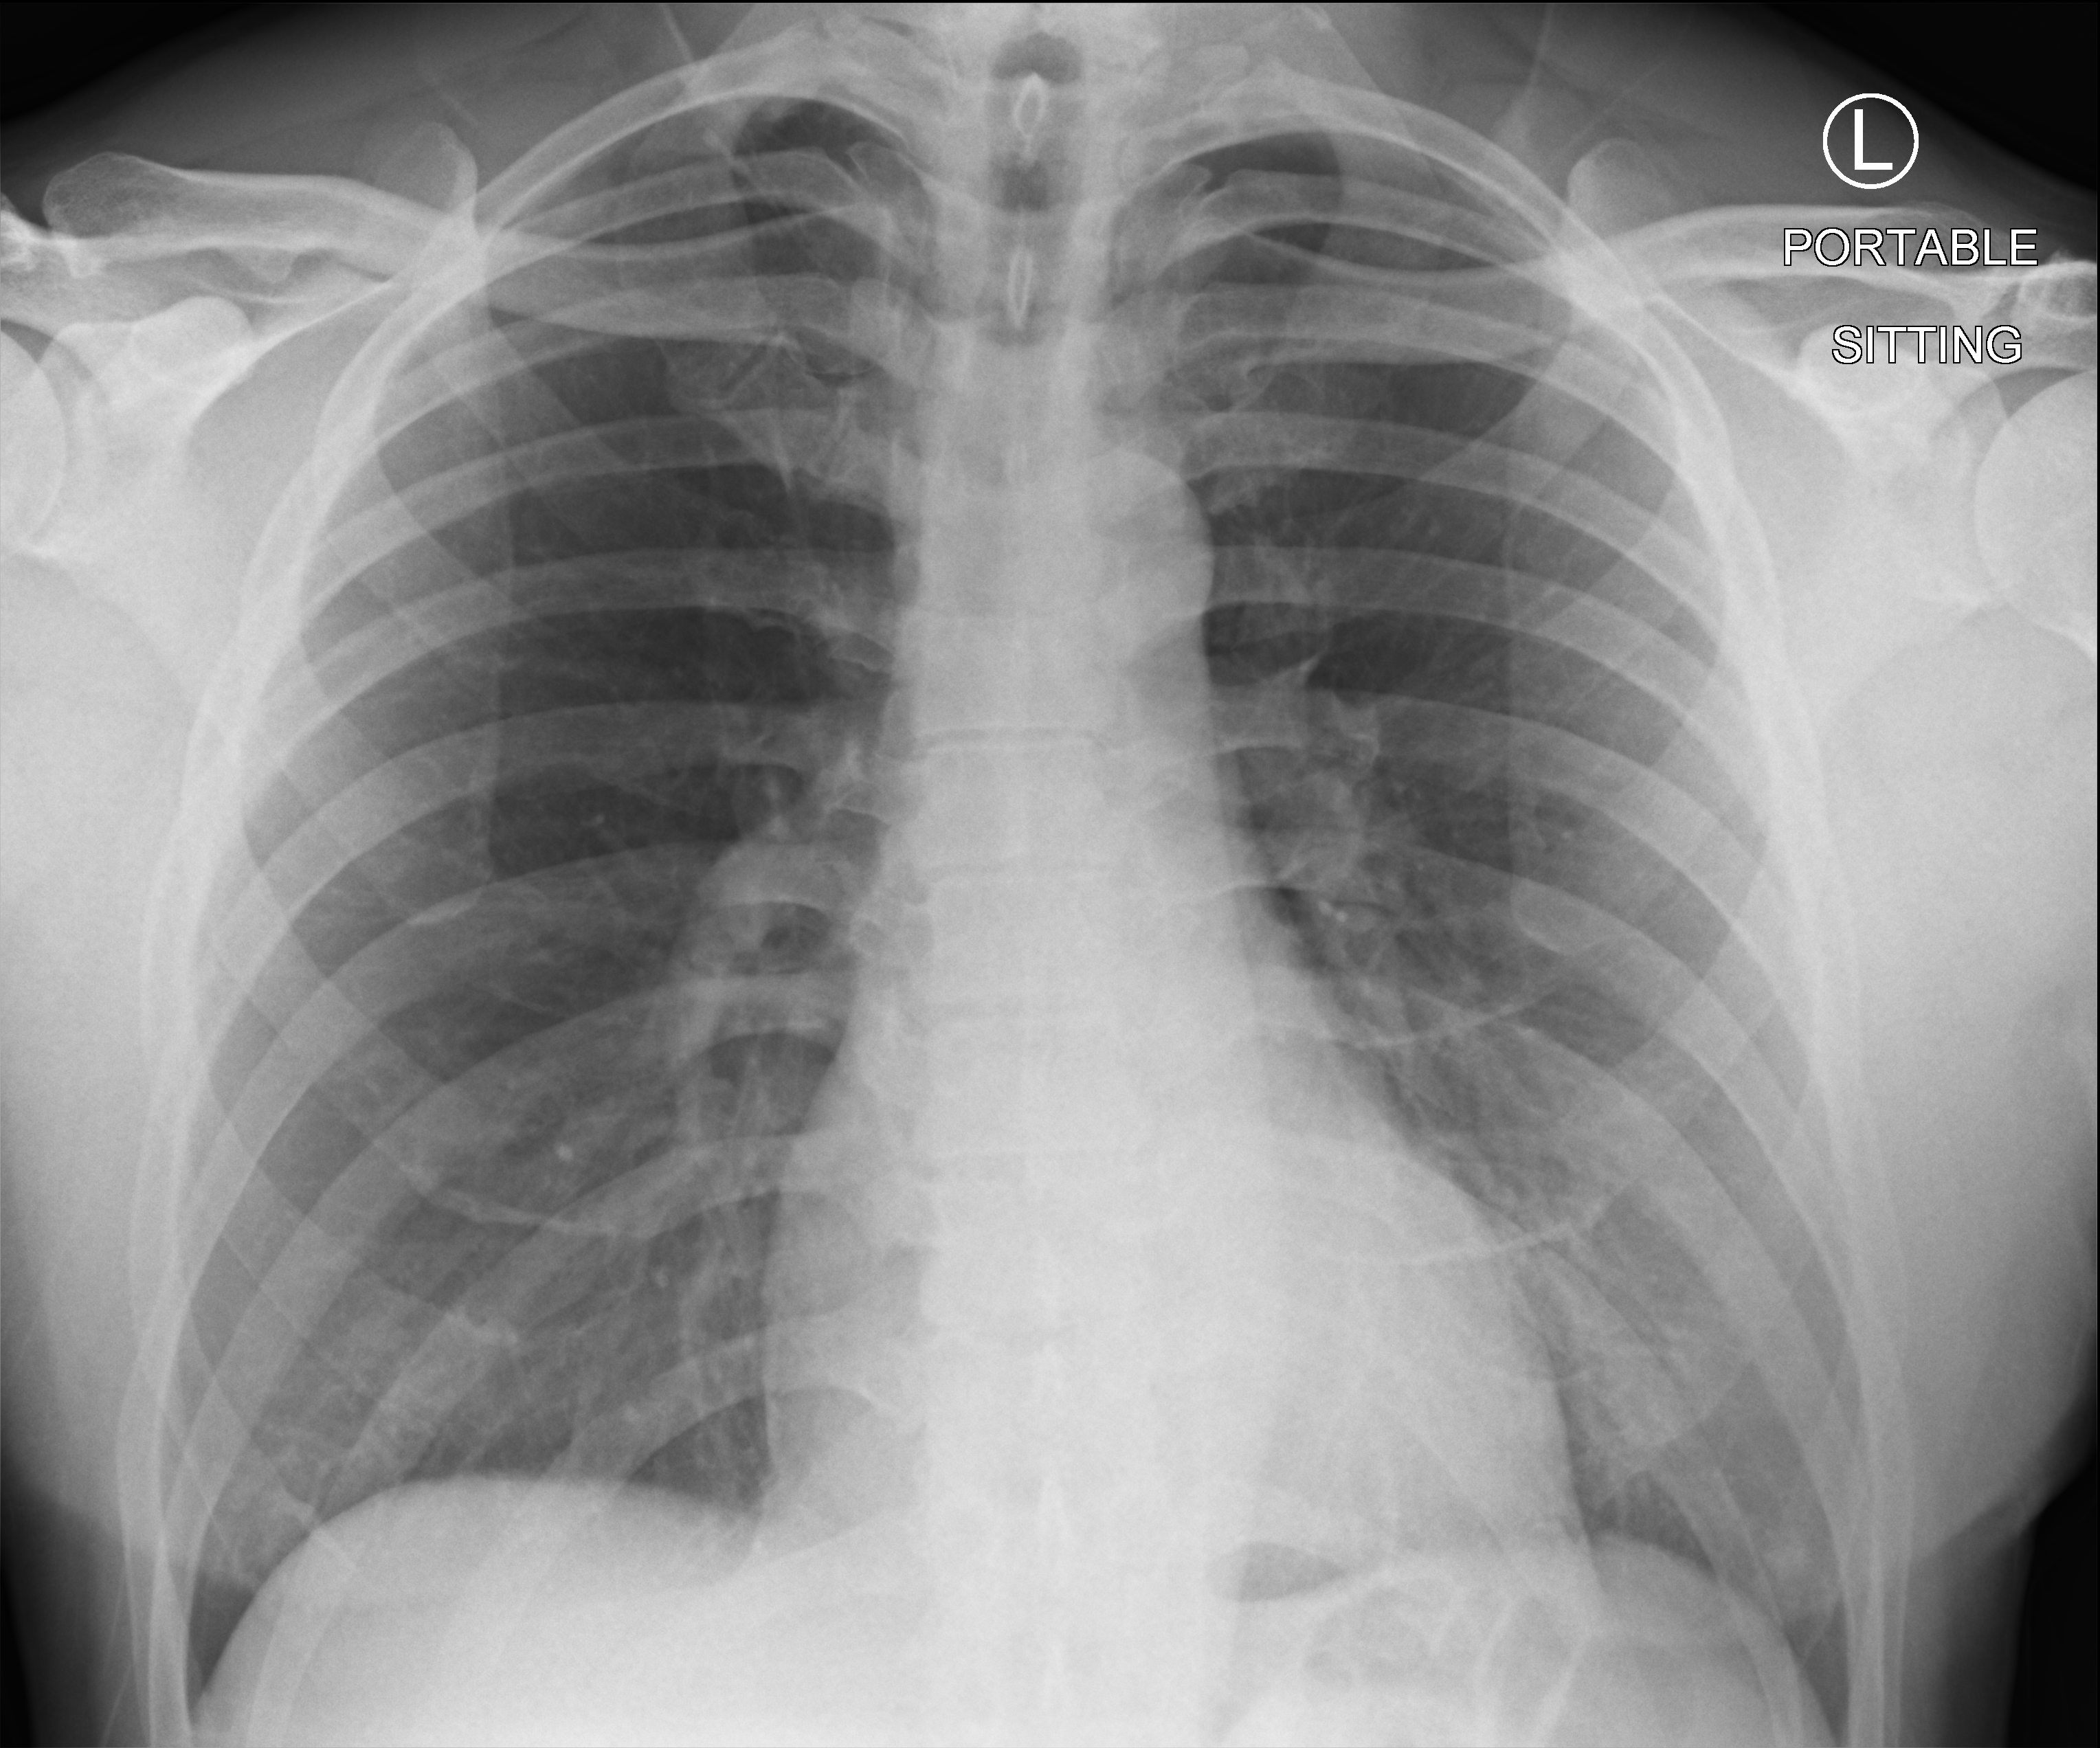
Bedside chest radiograph (computed radiography), anteroposterior (AP) projection. Male patient hospitalised with COVID-19, age 18–59 years.
Admission-level facts for this patient (not findings on this image; timing relative to this image not recorded): mechanically ventilated during this hospital stay: no; admitted to intensive care during this hospital stay: no.